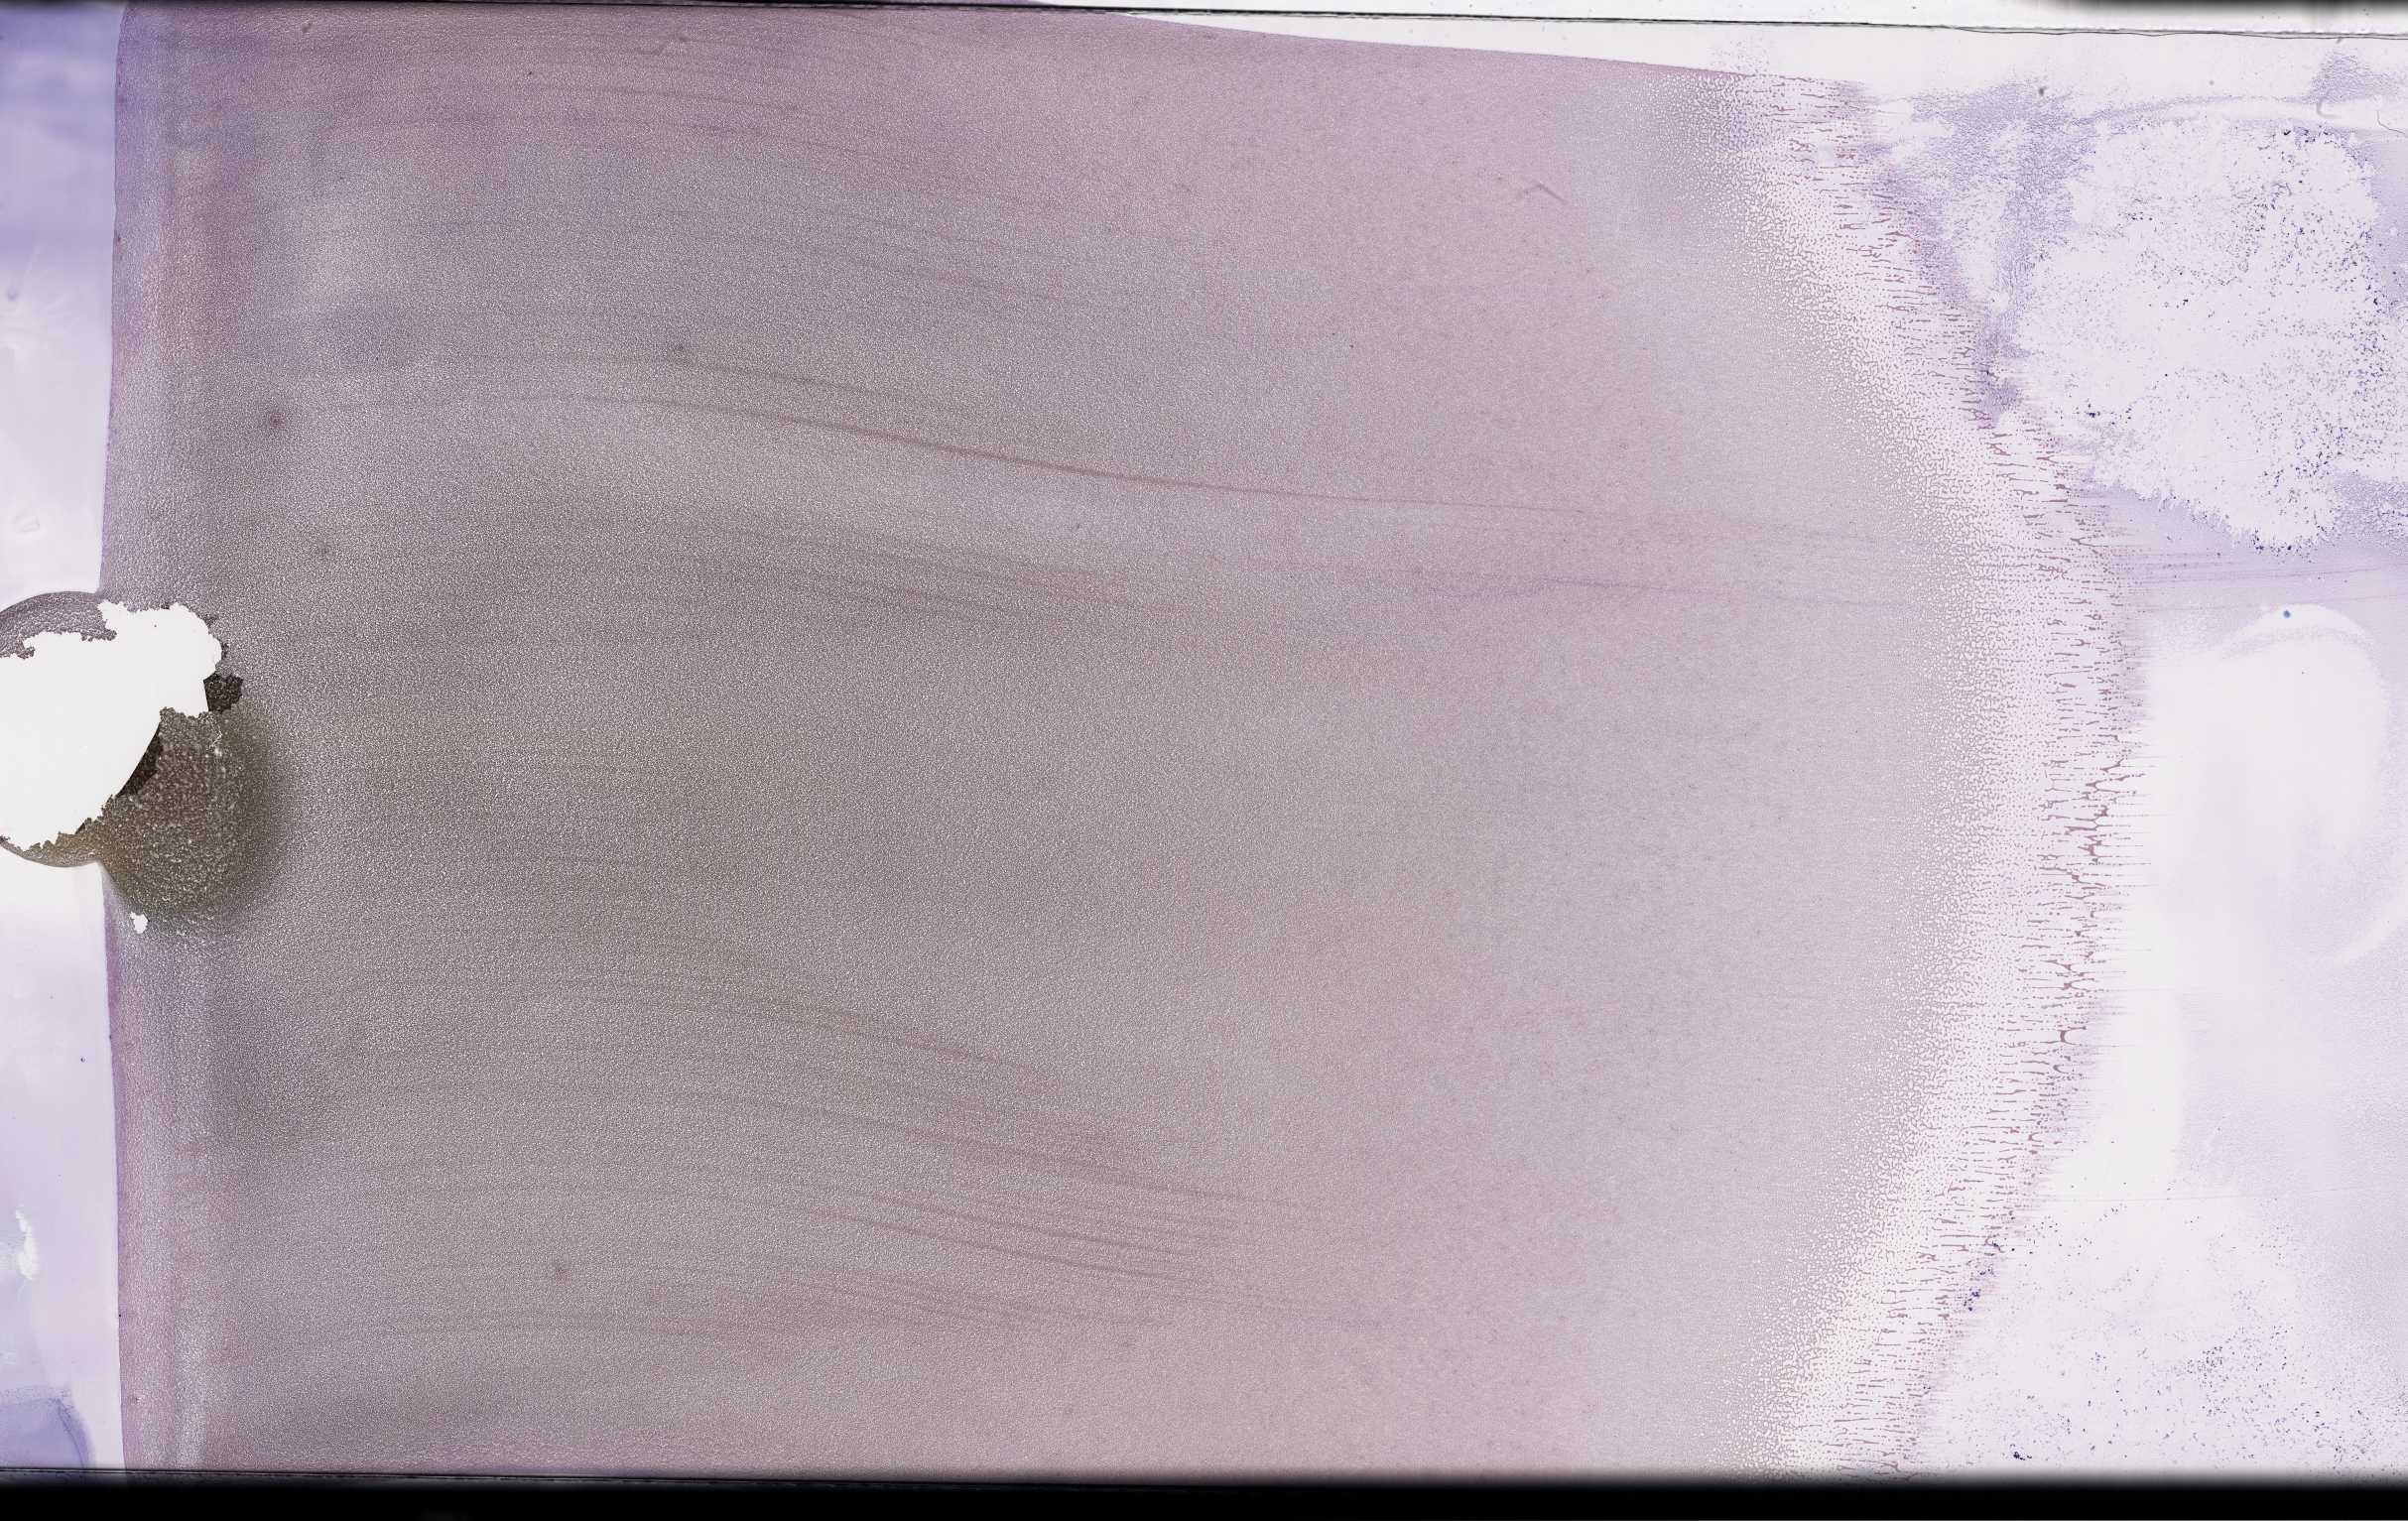
Wright-Giemsa-stained whole blood smear, whole-slide image — shown as a low-resolution overview of the whole scanned area (about 39.2 x 24.8 mm). EDTA-anticoagulated smear. Collected on treatment. Patient sex: male.
* from a patient with: Plasma Cell Myeloma